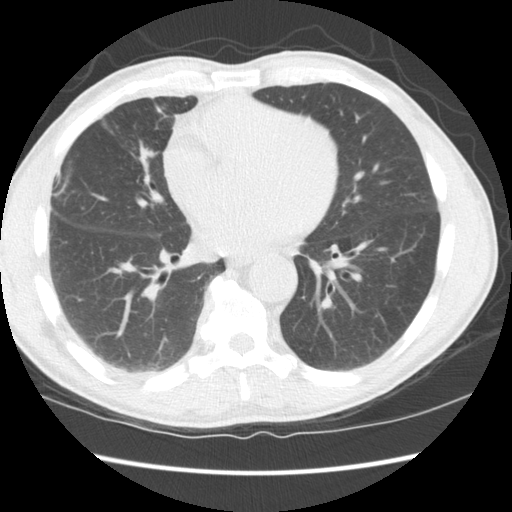
Low-dose screening chest CT, one axial slice. Slice 62 of 147 in the series (ordered by position). Reconstruction kernel STANDARD. Lung window (W 1500 / L -600 HU). 2.5 mm slice thickness. 512 × 512 image matrix, field of view 345 × 345 mm.
Structures marked on this image (outlined manually by an expert reader):
- lesion 1 (tumor, middle lobe of right lung): bounding box (x1, y1, x2, y2) in pixels: (146, 151, 153, 156)